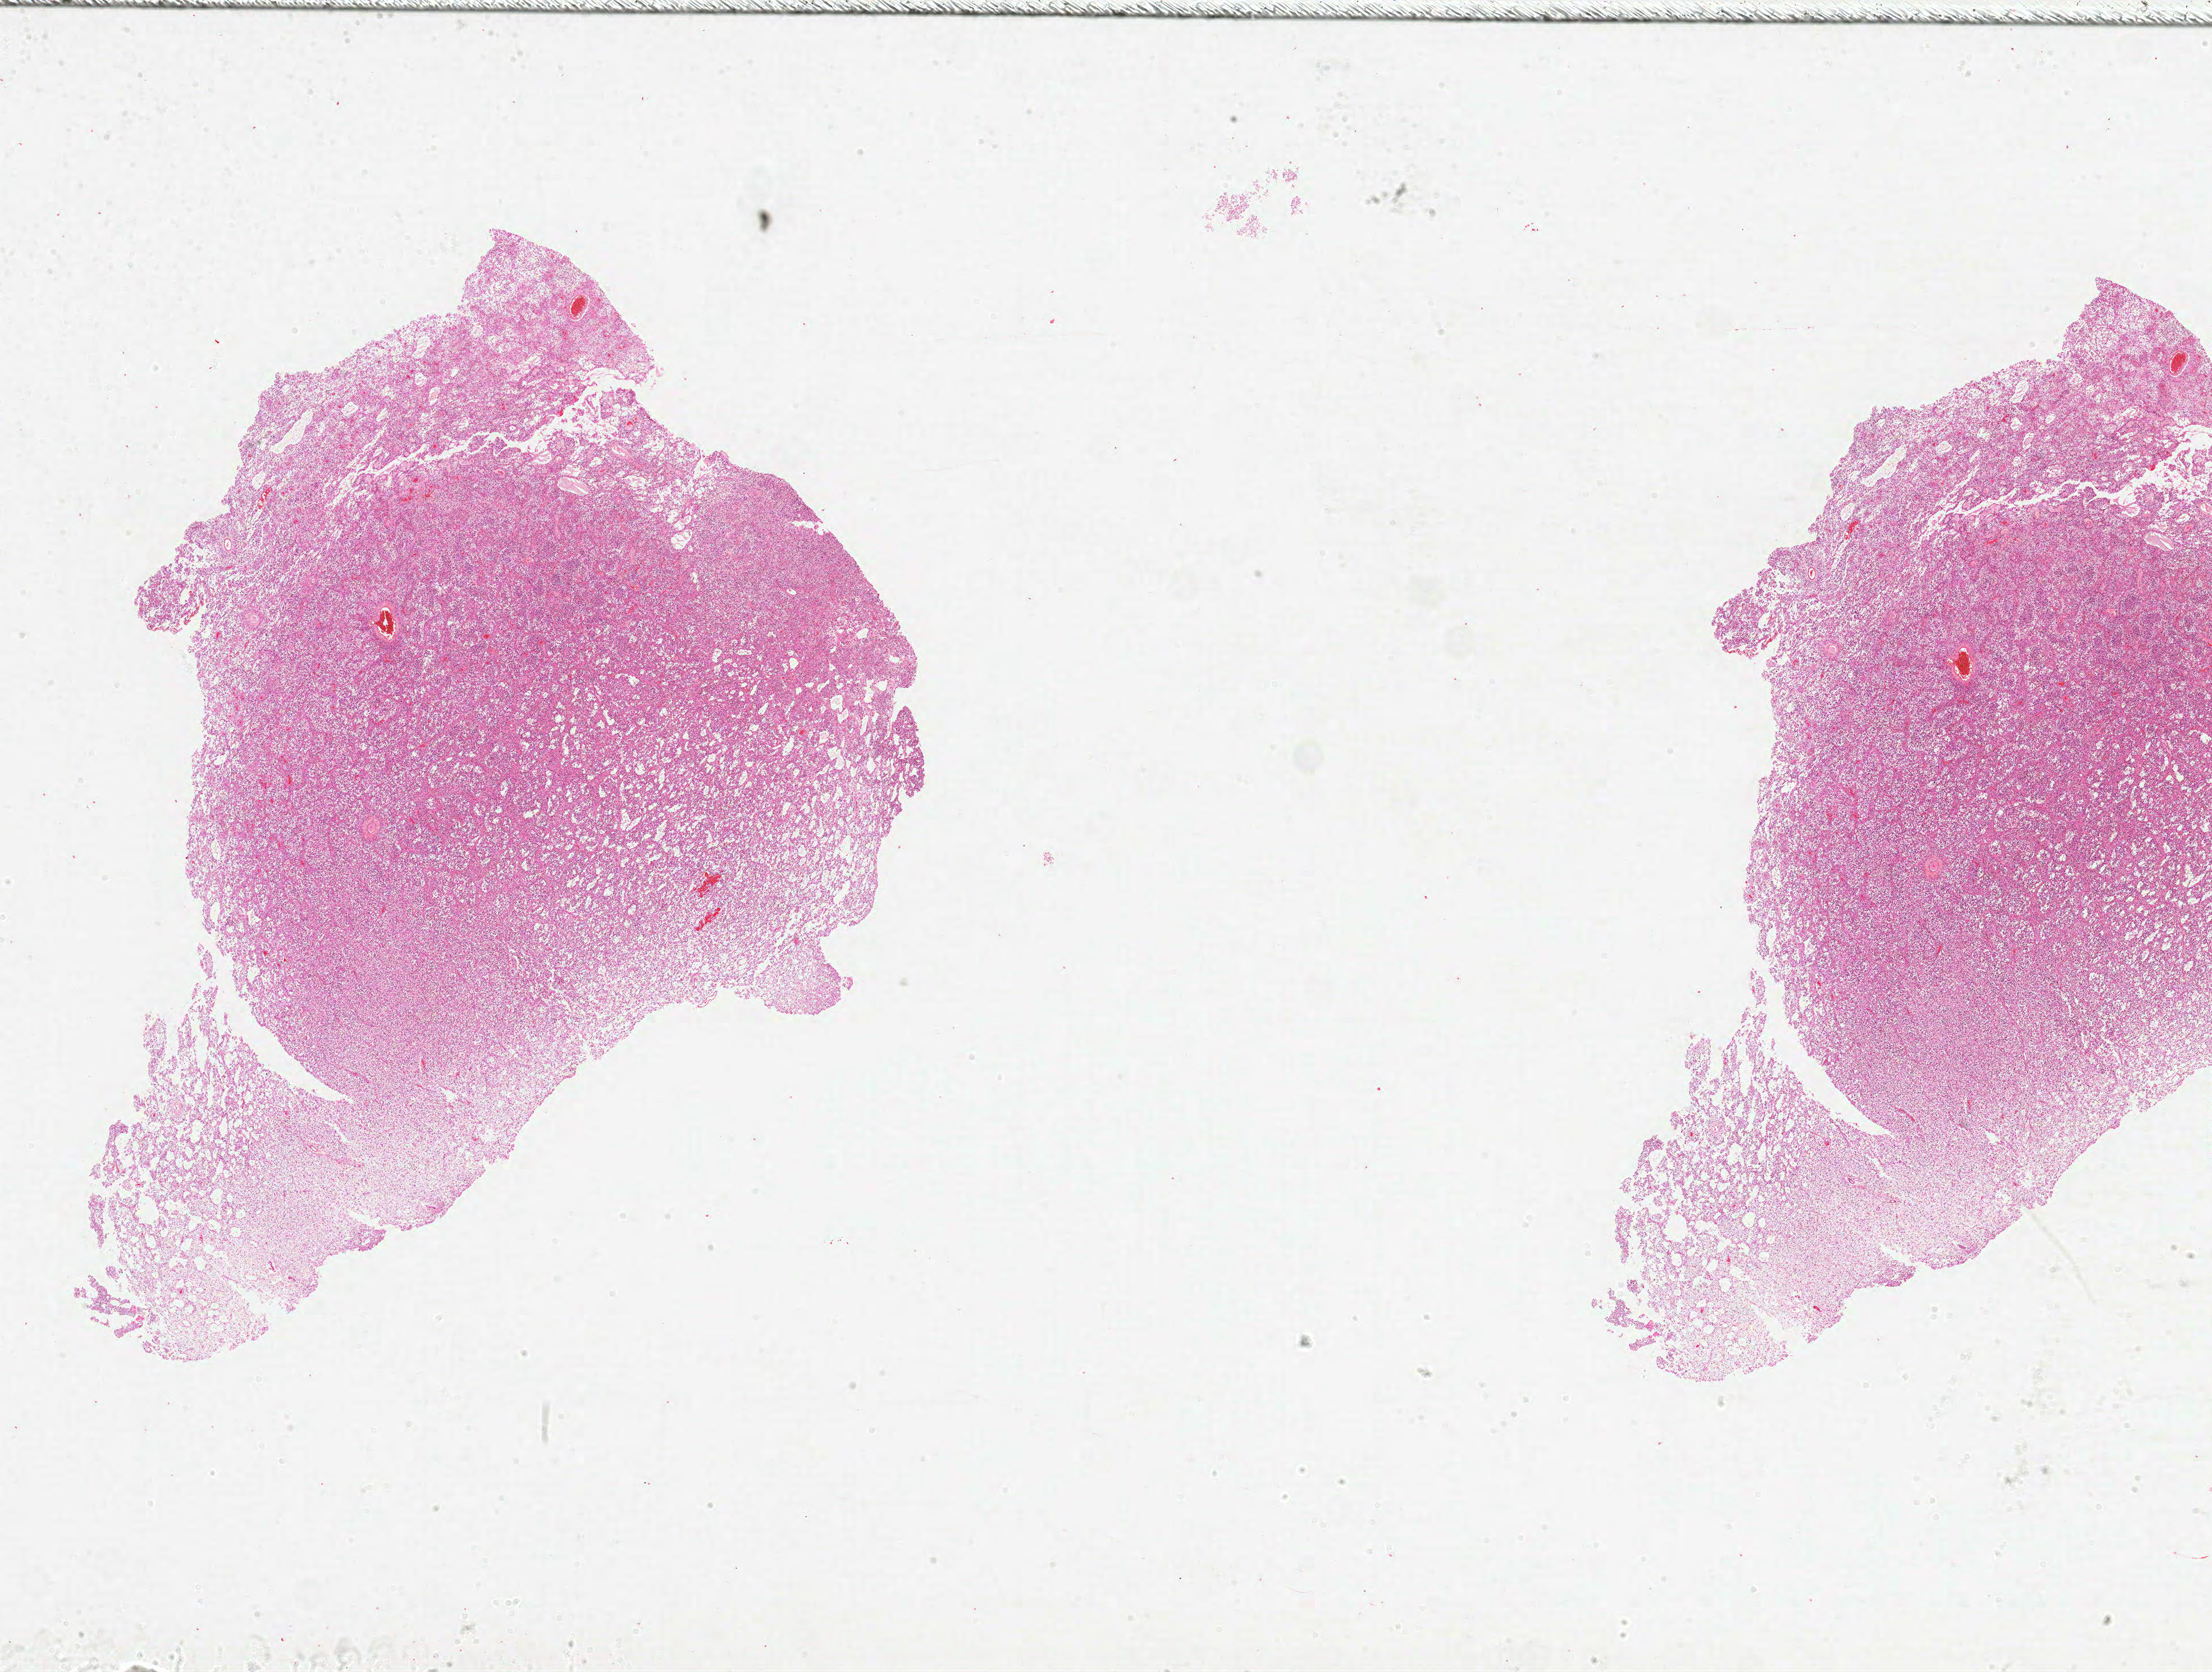
Whole-slide histology image, Hematoxylin and eosin (H&E) stained, shown as a low-resolution overview of the whole scanned area (about 31.0 x 23.4 mm, from a 20x scan); FFPE section; brain, primary tumour sample. Female, age 45 years at initial diagnosis.
• pathologic diagnosis: Glioblastoma